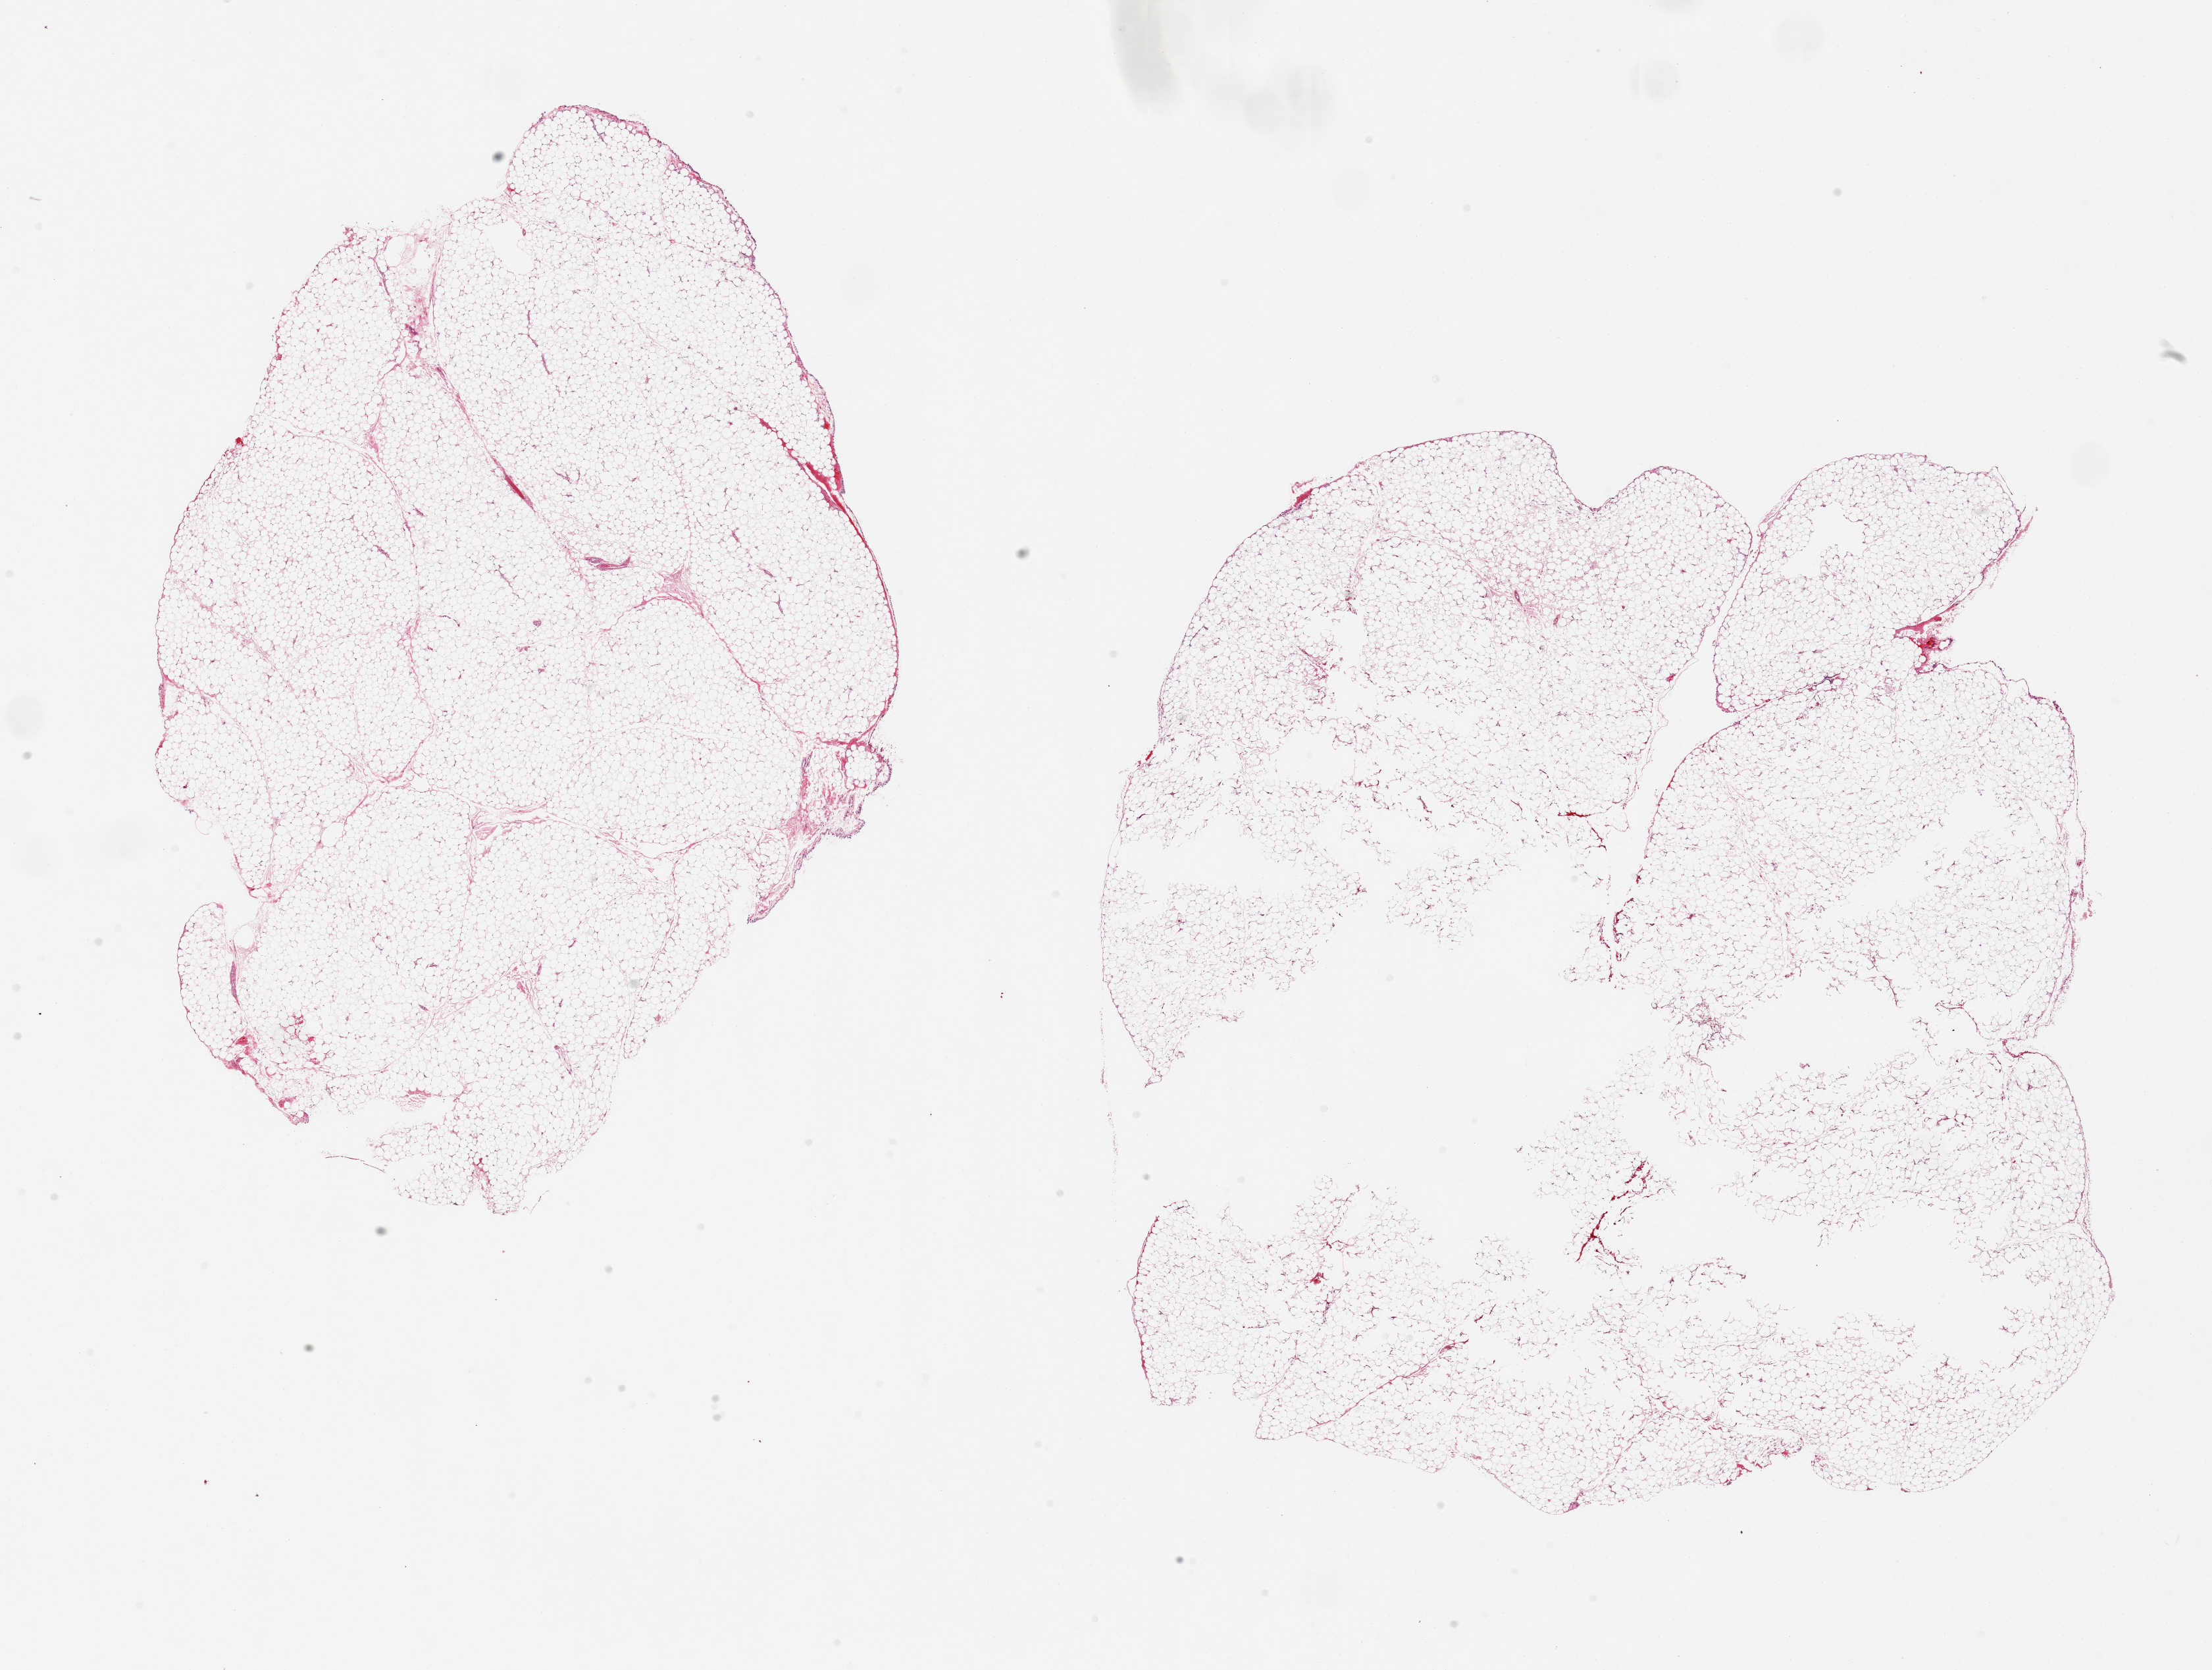
Digitized H&E-stained section, brightfield, a low-resolution overview of the entire scanned area, about 26.6 x 20.1 mm (slide scanned at 20x), PAXgene-fixed paraffin-embedded (PFPE) section, sampled site (target tissue): omentum, donor tissue sample. Donor sex: male.
Review note (as recorded): 2 pieces, minimal fascia/vascular elements present.